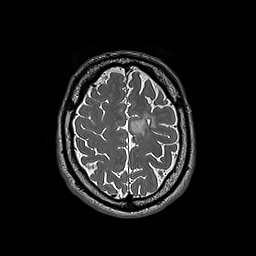
Brain MRI from a brain-tumour surgery series, one axial slice; position 53 of 192 along the scan axis; 1 mm slice thickness; 256 × 256 image matrix, field of view 250 × 250 mm. From the clinical record (not read from this slice): histopathology: Oligodendroglioma; WHO grade: 3; IDH mutation: yes.
Annotated regions visible in this slice (expert manual segmentation):
- tumour: bounding box <131,115,156,135> (left, top, right, bottom; pixels)